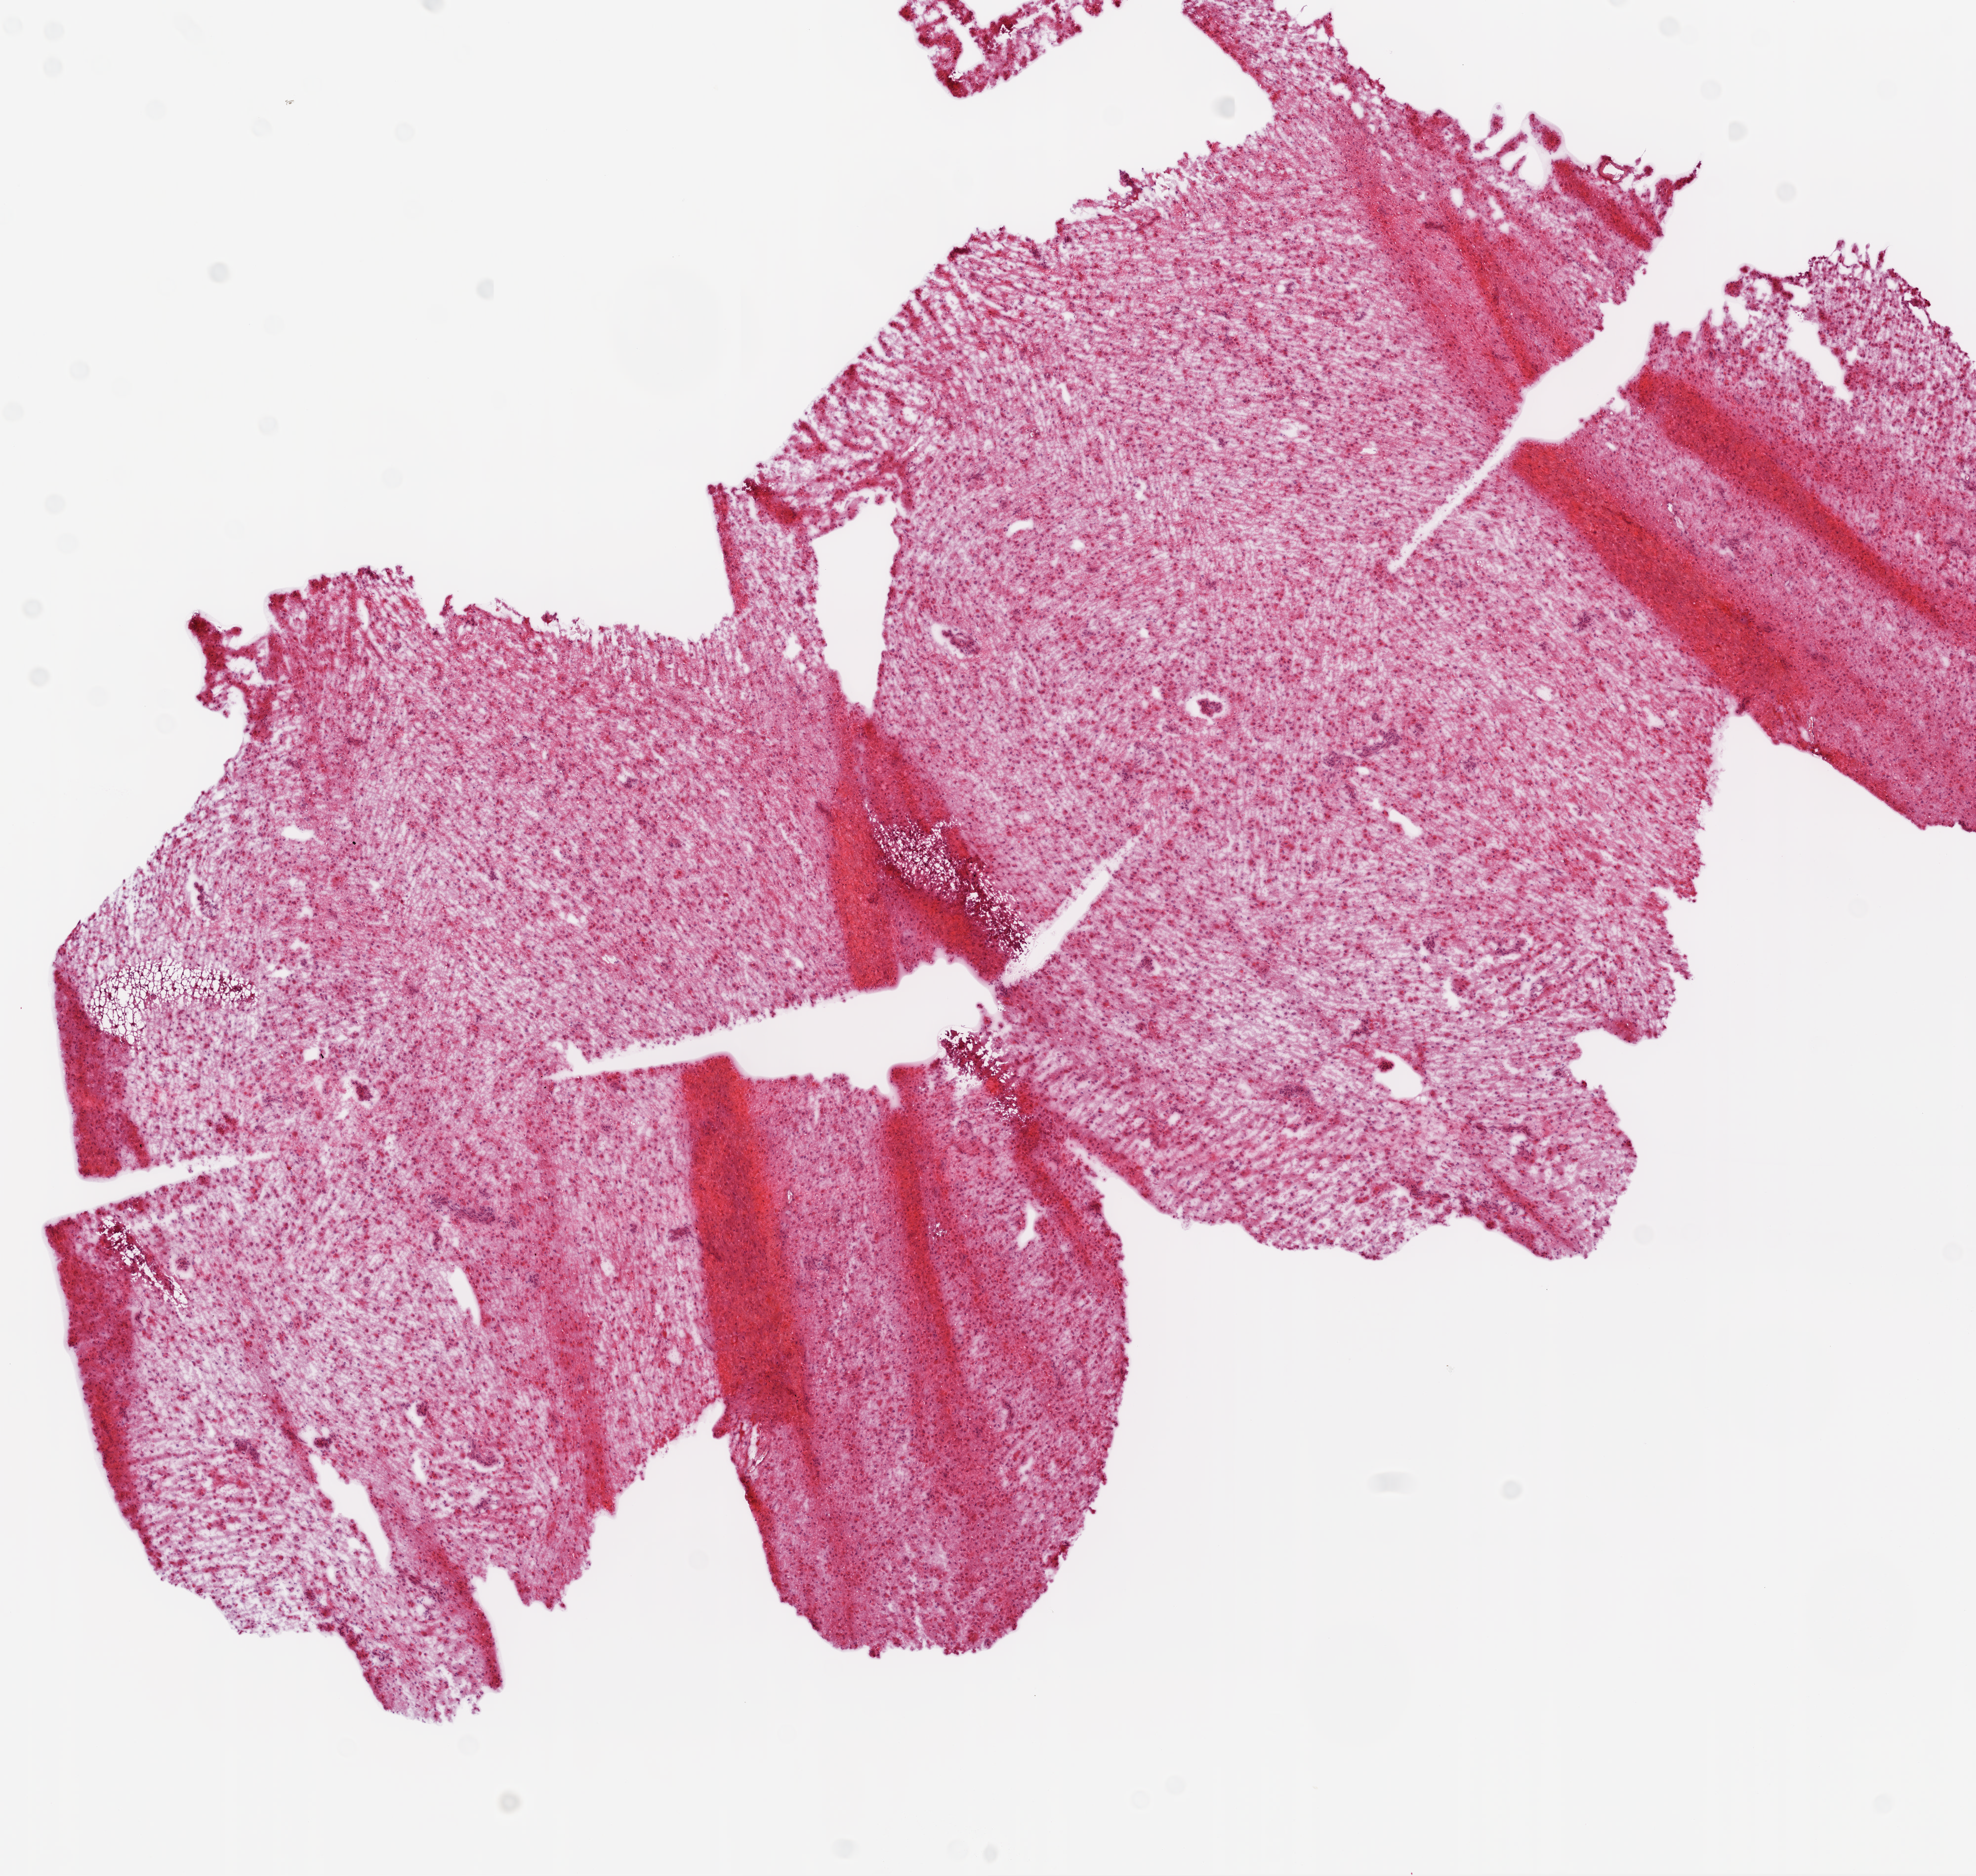
Digitized Hematoxylin and eosin (H&E) stained tissue section (whole slide) — a low-resolution overview of the entire scanned area, about 8.0 x 7.6 mm (acquisition: 20x scan), frozen section, brain, primary tumour sample. Female, age 36 years at initial diagnosis.
Diagnosis: Glioblastoma.